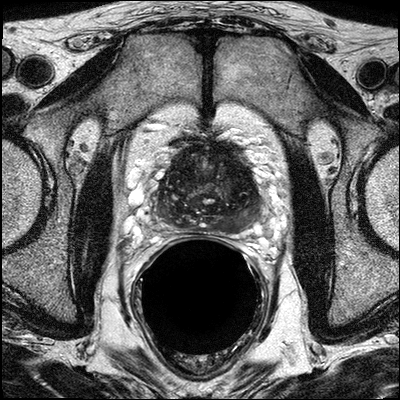
MRI of the prostate; 3 images, each a single mid-volume slice chosen by position (not for content). Treatment context recorded for this patient: No surgery, Casodex, ADT and XRT.
Image 1: axial T2-weighted image, series "T2W_TSE_AX", slice 17 of 32, 3 mm slice thickness.
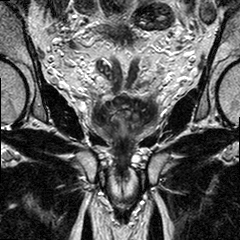
Image 2: T2-weighted coronal slice, series "T2W_TSE_COR", slice 14 of 26, 3 mm slice thickness.
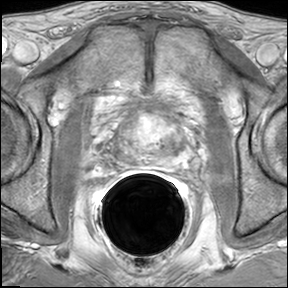
Image 3: axial dynamic contrast-enhanced (DCE) T1-weighted image, series "AX BLISS_GAD_8", slice 17 of 32, dynamic phase 5 of 8, 6 mm slice thickness.
MRI report (verbatim):
2.7 cm dominant mass in the left prostate base, in the posterior lateral peripheral zone with imaging findings suggestive of beginning extracapsular extension posterior-posterior-lateral with proximity to the left neurovascular bundle (prostate base). Irregular signal and enhancement of the left seminal vesicle base (adjacent to the primary tumor/dominant mass with in the left prostate base) suggestive of beginning seminal vesicle infiltration. The seminal vesicles show bilateral atrophy, and do not show regular thin walled fluid filled vesicles on either side. The left seminal vesicles base; the vesicles which are directly superior and adjacent to the tumor within left posterior lateral prostate show suspicious enhancement on the contrast enhanced images. Imaging findings suggestive for seminal vesicles infiltration. No evidence of involvement of bladder neck and rectal wall. No suspiciously enlarged obturator and iliac lymph nodes.

Biopsy pathology report for this patient (as recorded):
PROSTATE BIOPSY
A. LEFT APEX: PROSTATIC ADENOCARCINOMA, GLEASON SCORE 4+3=7/10, INVOLVING ONE CORE, ABOUT 35% OF THE TISSUE SUBMITTED. B. LEFT LATERAL APEX:
PROSTATIC ADENOCARCINOMA, GLEASON SCORE 4+3=7/10, INVOLVING ONE CORE, ABOUT 5% OF THE TISSUE SUBMITTED. C. RIGHT APEX: BENIGN PROSTATIC TISSUE, NO TUMOR IDENTIFIED.
D. RIGHT LATERAL APEX: BENIGN PROSTATIC TISSUE, NO TUMOR IDENTIFIED.
E. LEFT MID: PROSTATIC ADENOCARCINOMA, GLEASON SCORE 4+3=7/10, INVOLVING ONE CORE, ABOUT 15% OF THE TISSUE SUBMITTED. F. LEFT LATERAL MID: PROSTATIC ADENOCARCINOMA, GLEASON SCORE 4+3=7/10, INVOLVING ONE CORE, ABOUT 30% OF THE TISSUE SUBMITTED. G. RIGHT MID: BENIGN PROSTATIC TISSUE, NO TUMOR IDENTIFIED.
H. RIGHT LATERAL MID: BENIGN PROSTATIC TISSUE, NO TUMOR IDENTIFIED. I. LEFT BASE: PROSTATIC ADENOCARCINOMA, GLEASON SCORE 4+3=7/10, INVOLVING ONE CORE, ABOUT 40% OF THE TISSUE SUBMITTED. J. LEFT LATERAL BASE: PROSTATIC ADENOCARCINOMA, GLEASON SCORE 4+3=7/10, INVOLVING ONE CORE, ABOUT 60% OF THE TISSUE SUBMITTED. K. RIGHT BASE:
BENIGN PROSTATIC TISSUE, NO TUMOR IDENTIFIED. L. RIGHT LATERAL BASE: BENIGN PROSTATIC TISSUE, NO TUMOR IDENTIFIED.